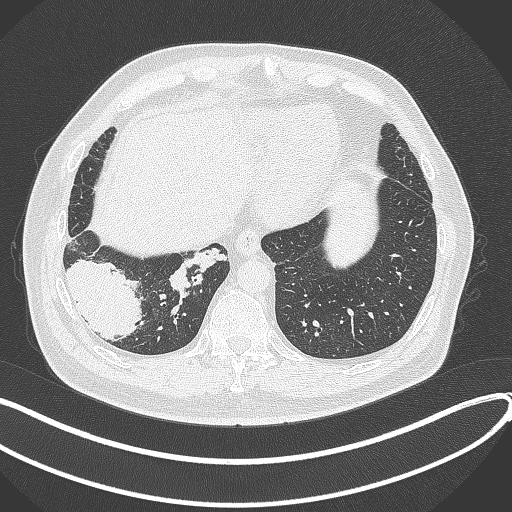
Chest CT, one axial slice; slice 76 of 360 in the series (ordered by position); 120 kVp; lung window (W 1500 / L -600 HU); 512 × 512 image matrix, field of view 400 × 400 mm. Patient: male, 59 years.
Outlined on this slice (rectangle marked by the reading radiologist):
- lung tumour (recorded histology: adenocarcinoma): bounding box [x1, y1, x2, y2] px = [62, 248, 149, 341]